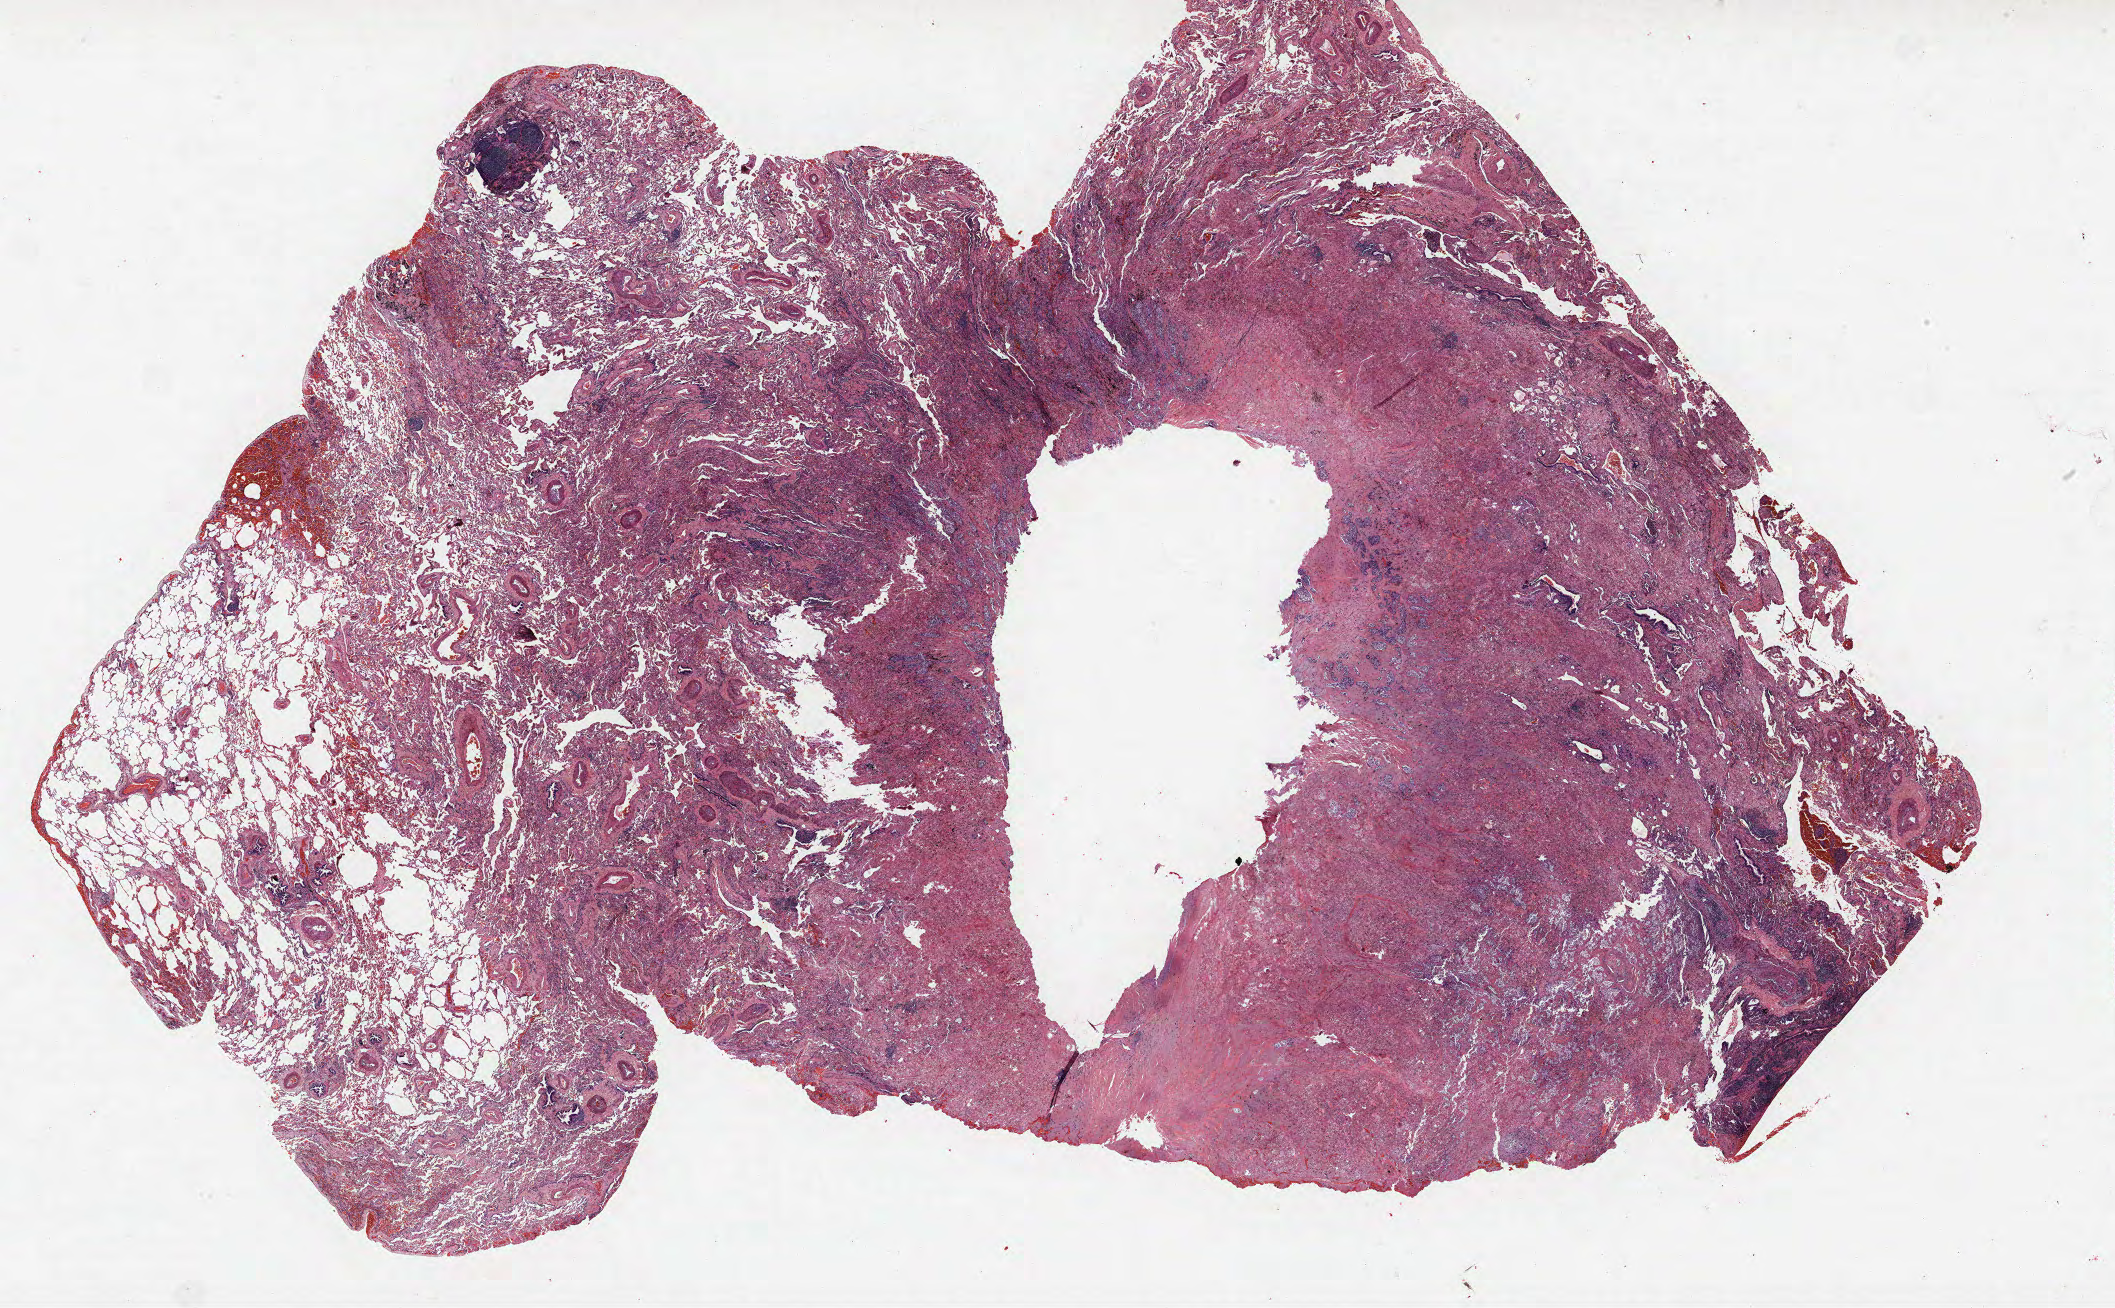
H&E-stained whole-slide image — low-resolution overview of the scanned area, about 33.8 x 20.9 mm (acquisition: 40x scan). Formalin-fixed paraffin-embedded (FFPE) section. Lung. Male patient, aged 59 at enrolment. Former smoker at enrolment. Grade: undifferentiated (G4).
- participant's lung-cancer diagnosis: Large cell carcinoma, NOS
- tumour size (pathology): 25 mm
- ICD-O-3 topography: upper lobe of lung (C34.1)
- stage (AJCC 6th edition): IA
- primary tumour location (clinical record): right upper lobe